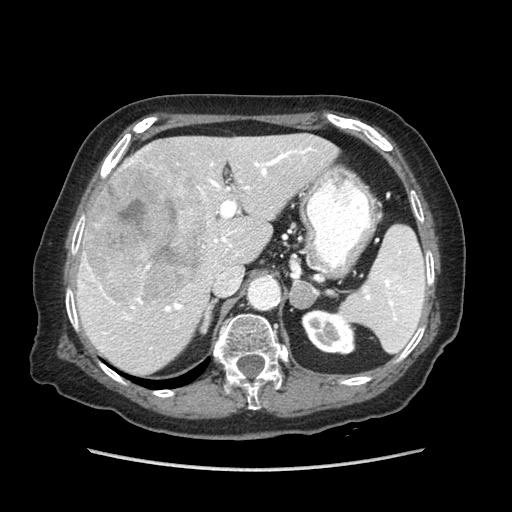
Contrast-enhanced abdominal CT (liver protocol), one axial slice. Slice 51 of 89 in the series (ordered by position). Soft-tissue window (W 400 / L 40 HU). 512 × 512 image matrix, field of view 360 × 360 mm. Case-level facts recorded for this patient, not image findings: diagnosis: hepatocellular carcinoma (patient treated with transarterial chemoembolisation; whether this scan precedes or follows treatment is not stated here); TNM stage (as recorded): Stage-IIIA; Child-Pugh class: A; tumour differentiation: well differentiated.
Outlined on this slice (semi-automatic segmentation, software-assisted and operator-edited):
- liver parenchyma outside the tumour (the mass and vessels are separate outlines, so this box may not span the whole liver): bounding box [x1, y1, x2, y2] px = [76, 134, 338, 374]
- mass: [85, 160, 210, 304]
- liver vessels: [80, 147, 313, 349]